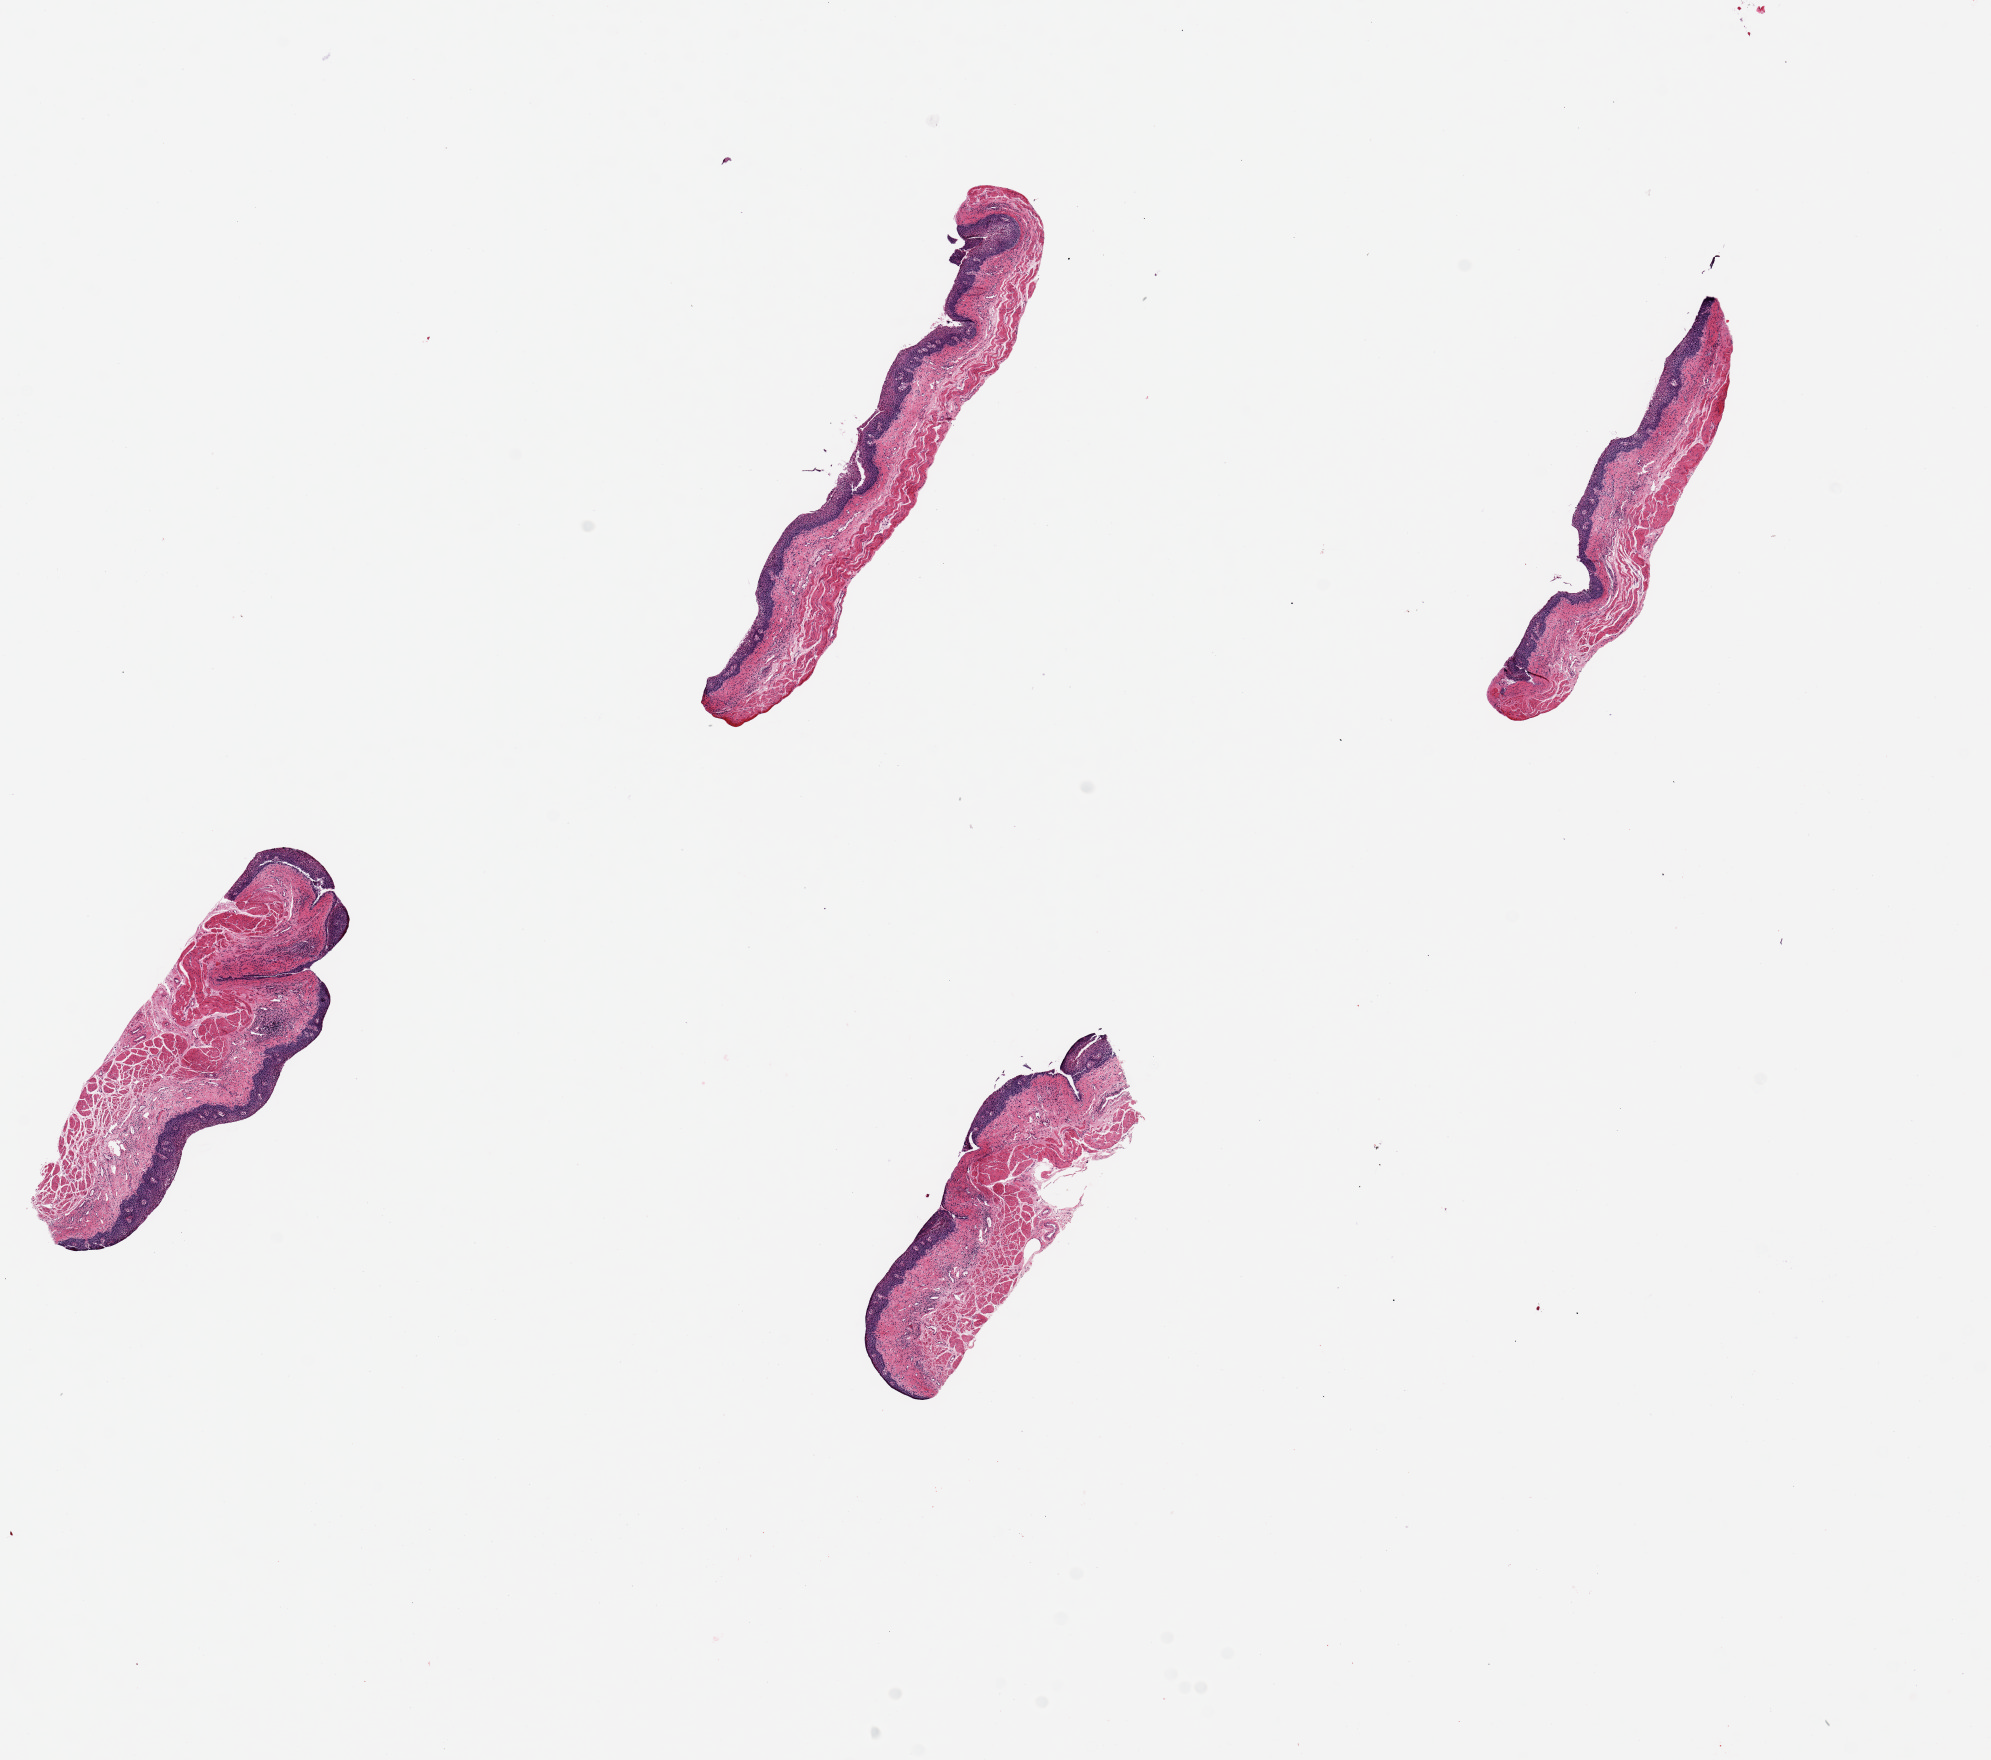
H&E whole-slide image — shown as a low-resolution overview of the whole scanned area (about 15.8 x 13.9 mm); PAXgene-fixed paraffin-embedded (PFPE) section; sampled site (target tissue): esophageal mucous membrane; donor tissue sample.
• review note (as recorded): 4 pieces, up to 5mm x 865um & 3.6x1.1 mm